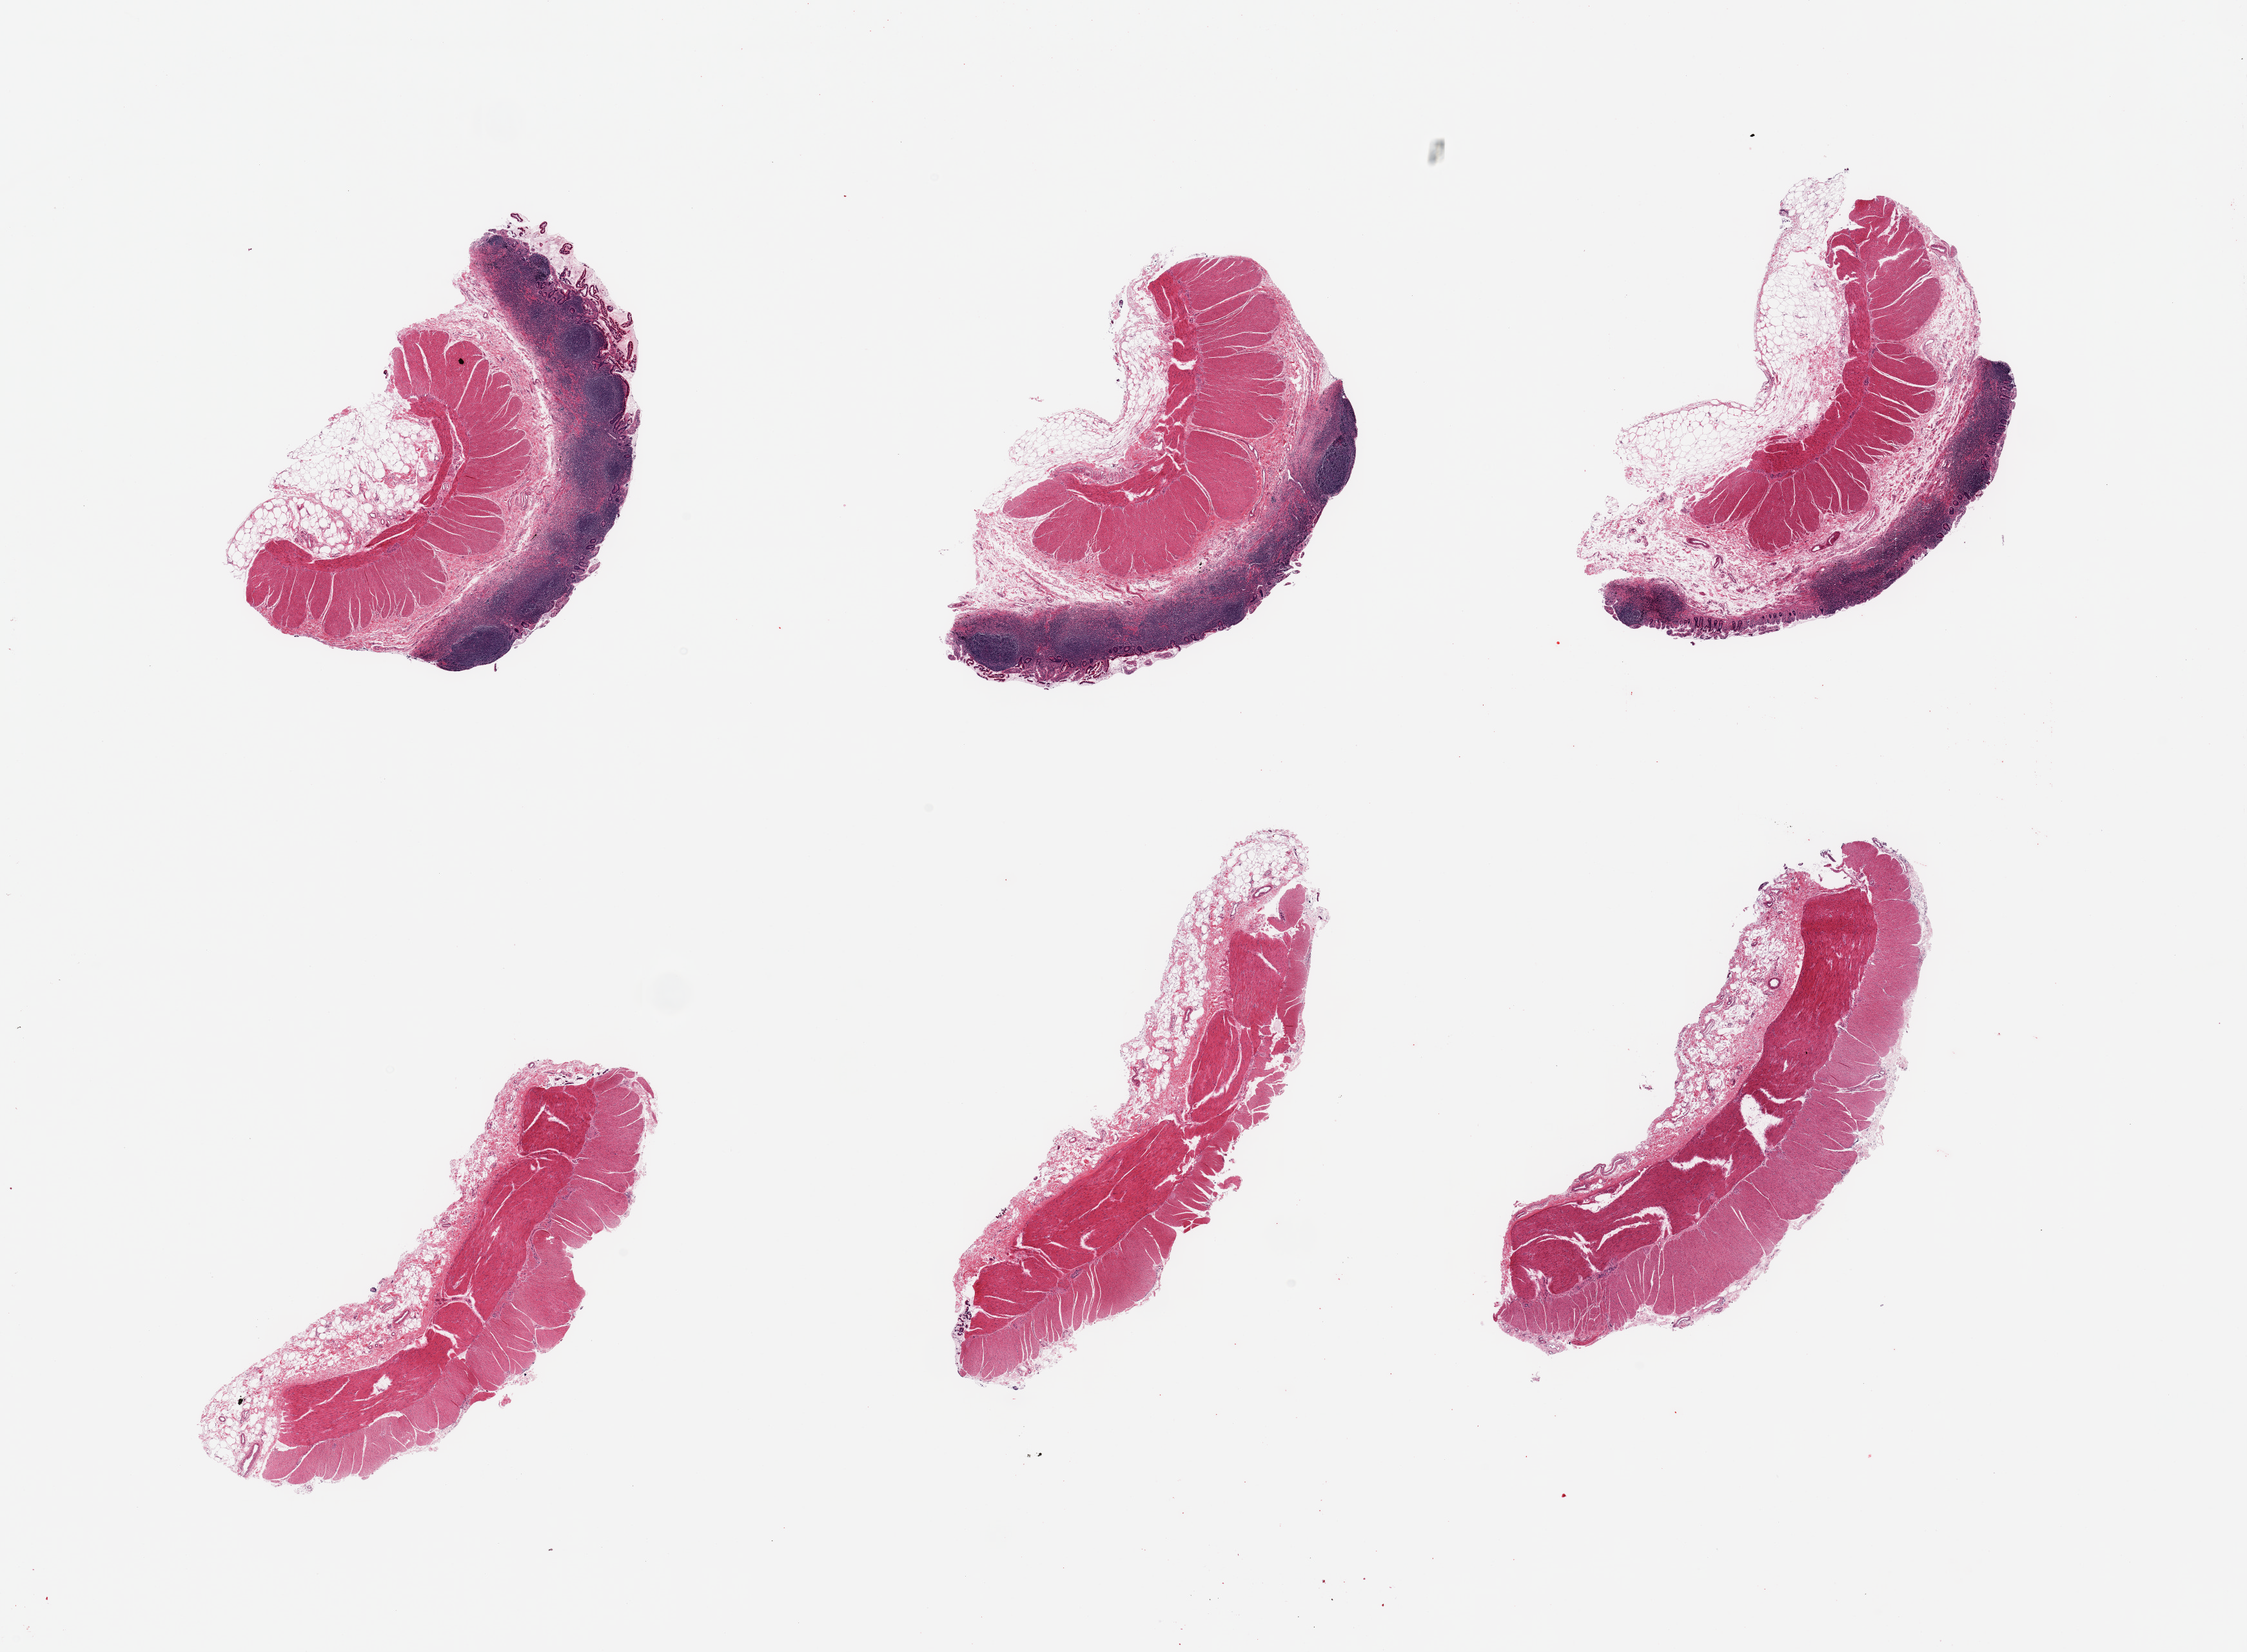
H&E whole-slide image — shown as a low-resolution overview of the whole scanned area (about 27.6 x 20.3 mm, acquisition: 20x scan). Donor: male.
Specimen: PAXgene-fixed, paraffin-embedded tissue; target tissue: ileum; donor tissue sample.